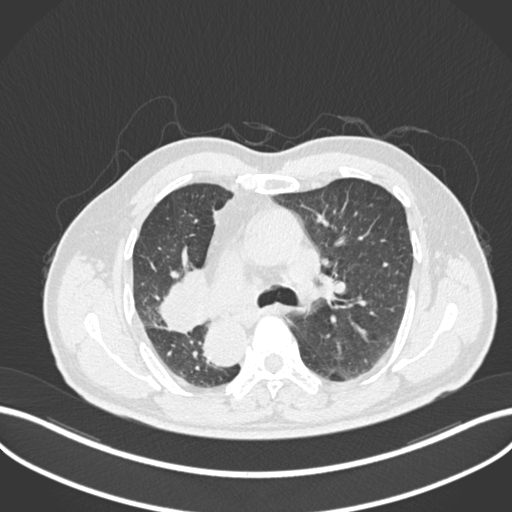
Chest CT, one axial slice; lung window (W 1500 / L -600 HU); 1 mm slice thickness; 512 × 512 image matrix. Male patient, age 67 years. From the clinical record (not read from this slice): clinical TNM (as recorded): T2a N0 M0.
Structures marked on this image (rectangle marked by the reading radiologist):
- lung tumour (recorded histology: squamous cell carcinoma): box from (x=155, y=262) to (x=210, y=335) px